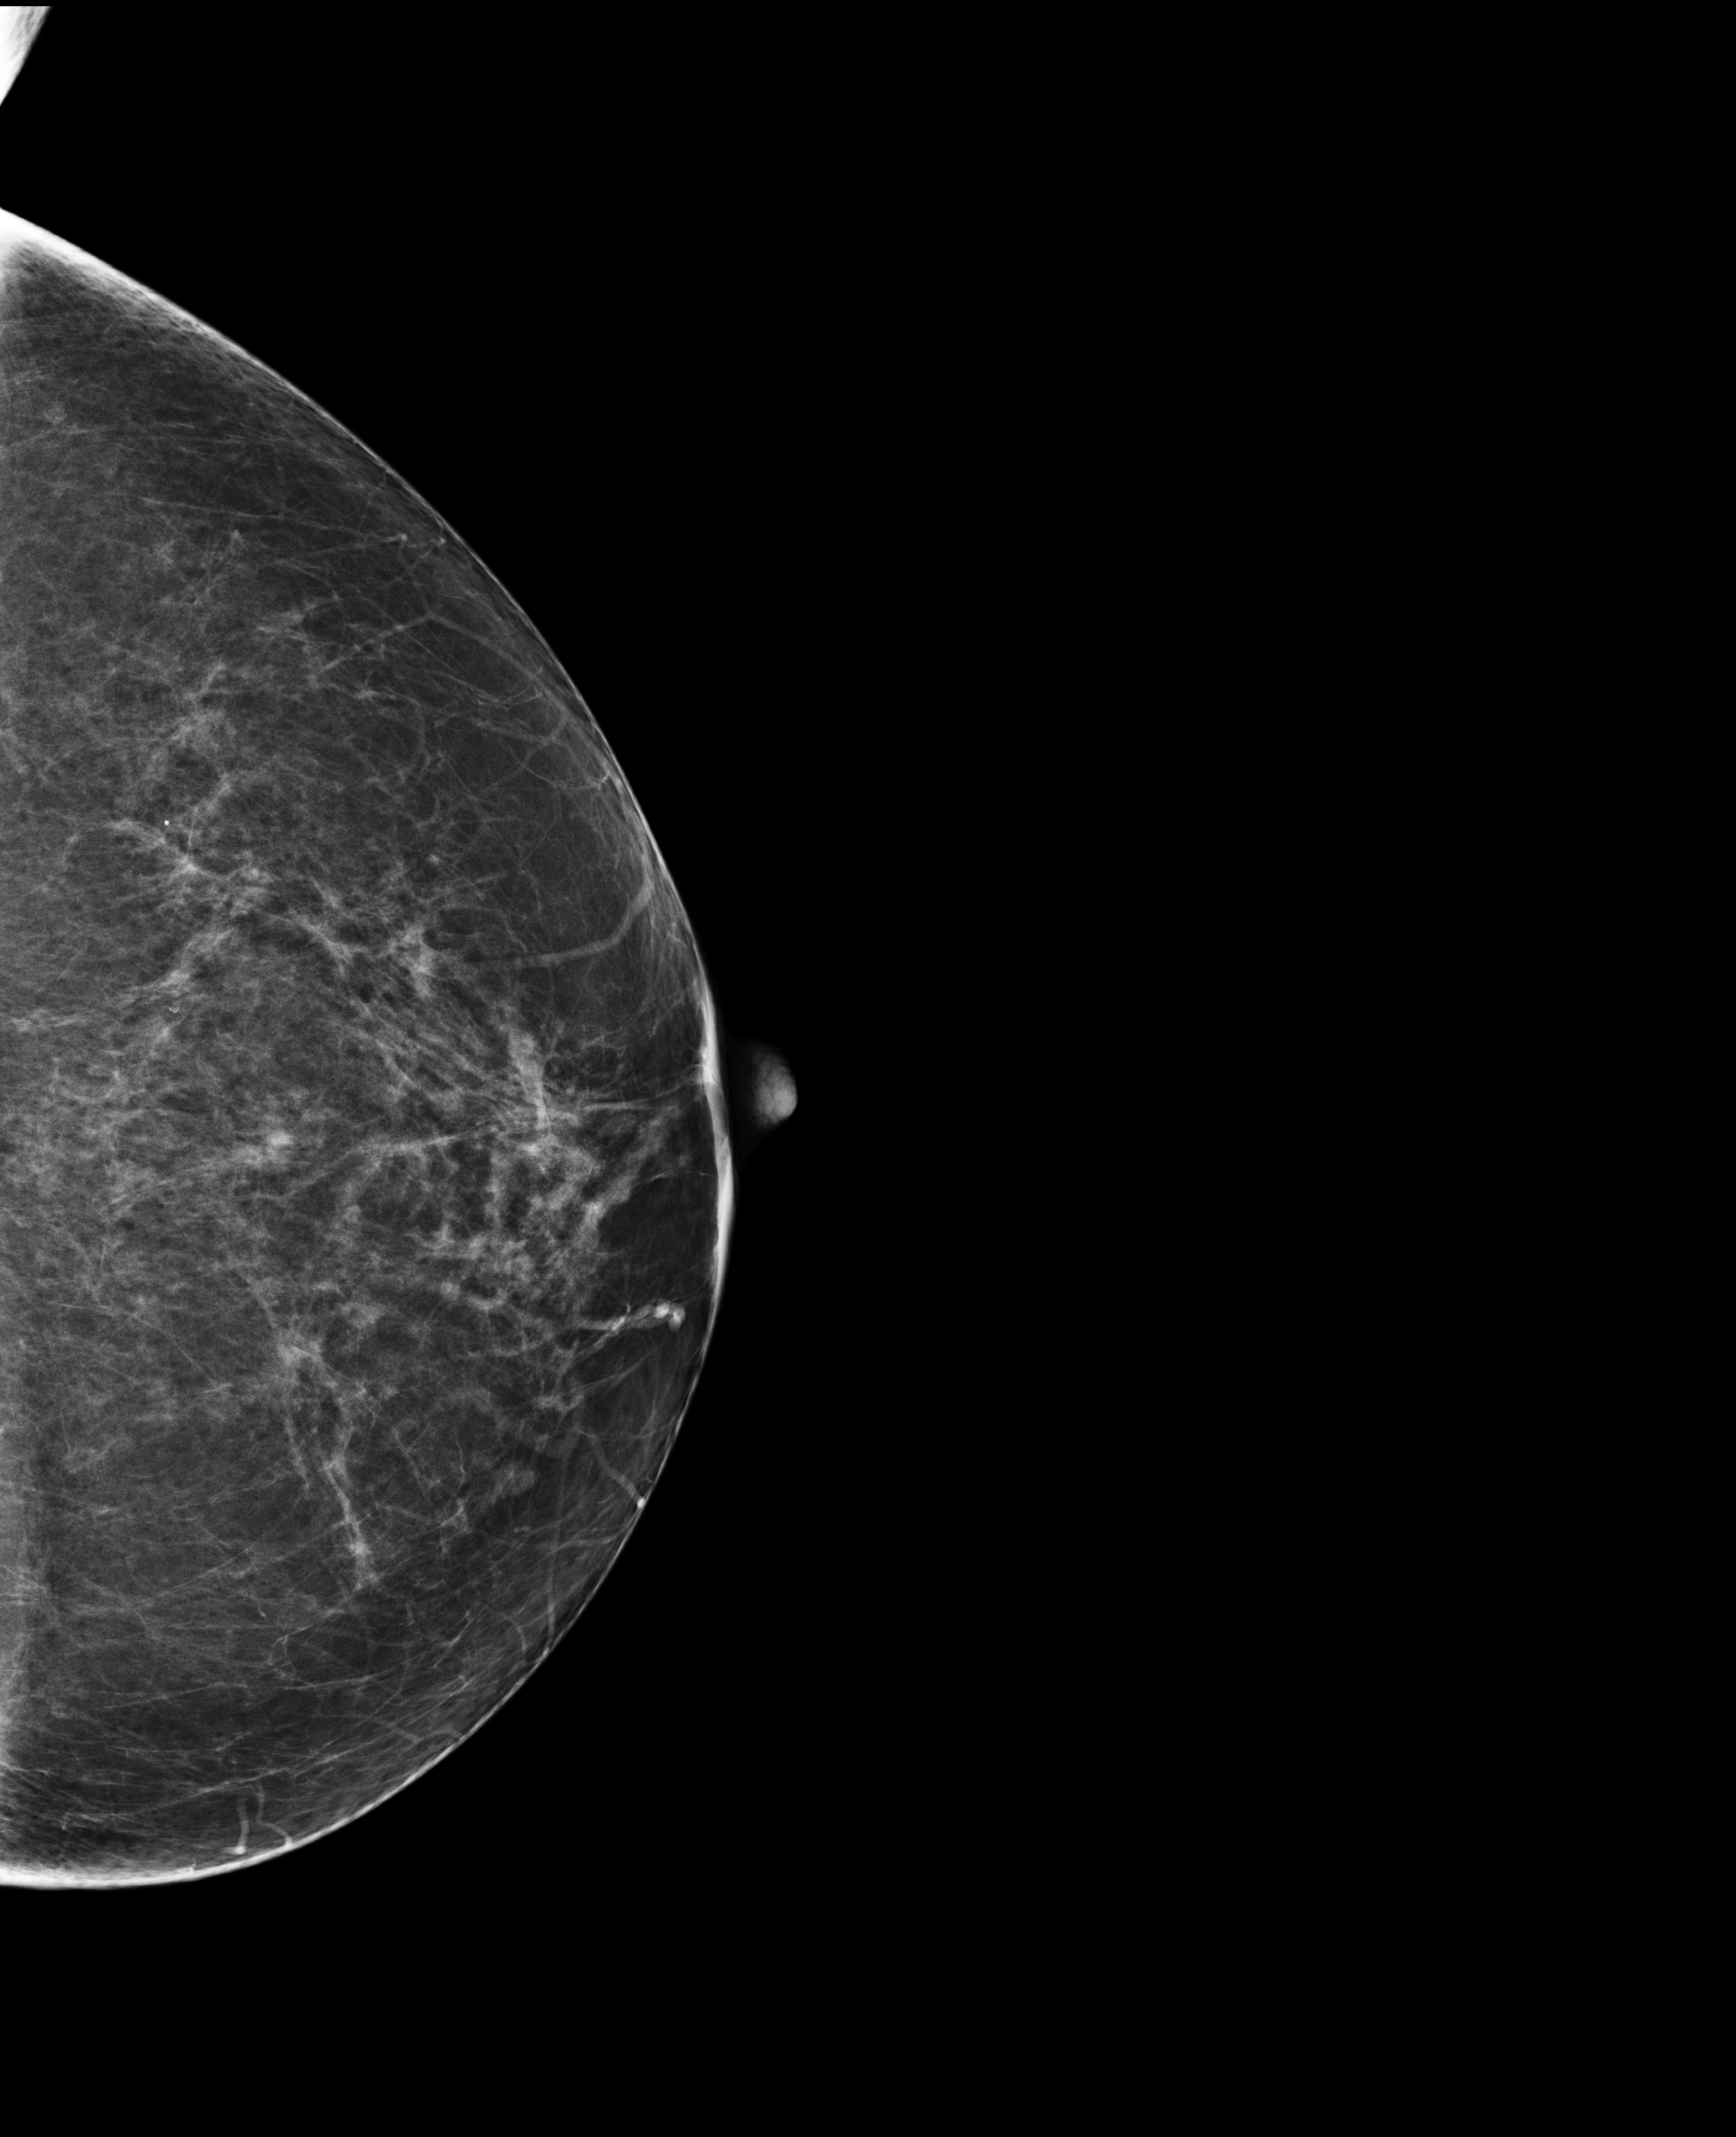
Digital mammogram (FFDM); left breast; craniocaudal (CC) view; annual screening mammography examination; system: Selenia Dimensions. Female patient, age 74 years.
BI-RADS breast density category at the screening exam (both breasts, scale 1–4): 3. Final BI-RADS category for the screening round (tomosynthesis exam, both breasts): category 4. Recall: recalled for additional imaging after this screen.